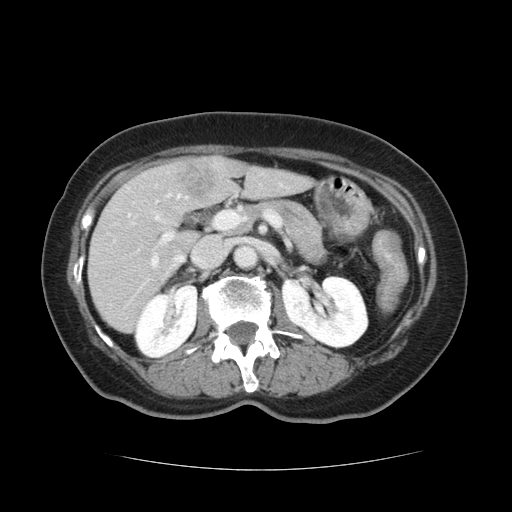
Contrast-enhanced abdominal CT, one axial slice. Position 58 of 128 along the scan axis. Intravenous contrast given. Soft-tissue window (W 400 / L 40 HU). 512 × 512 image matrix. Female patient, age 67 years. Case-level facts recorded for this patient, not image findings: diagnosis: colorectal cancer liver metastases, imaged before liver resection; multiple liver metastases: yes; largest metastasis: 3 cm; chemotherapy before resection: no.
Outlined on this slice (expert manual segmentation):
- hepatic veins: box from (x=173, y=254) to (x=184, y=266) px
- liver: (x=89, y=158)–(x=308, y=332)
- planned liver remnant (the part of the liver to remain after resection): (x=89, y=166)–(x=309, y=332)
- portal vein (with intrahepatic branches): (x=133, y=213)–(x=237, y=267)
- liver metastasis: (x=177, y=164)–(x=217, y=201)